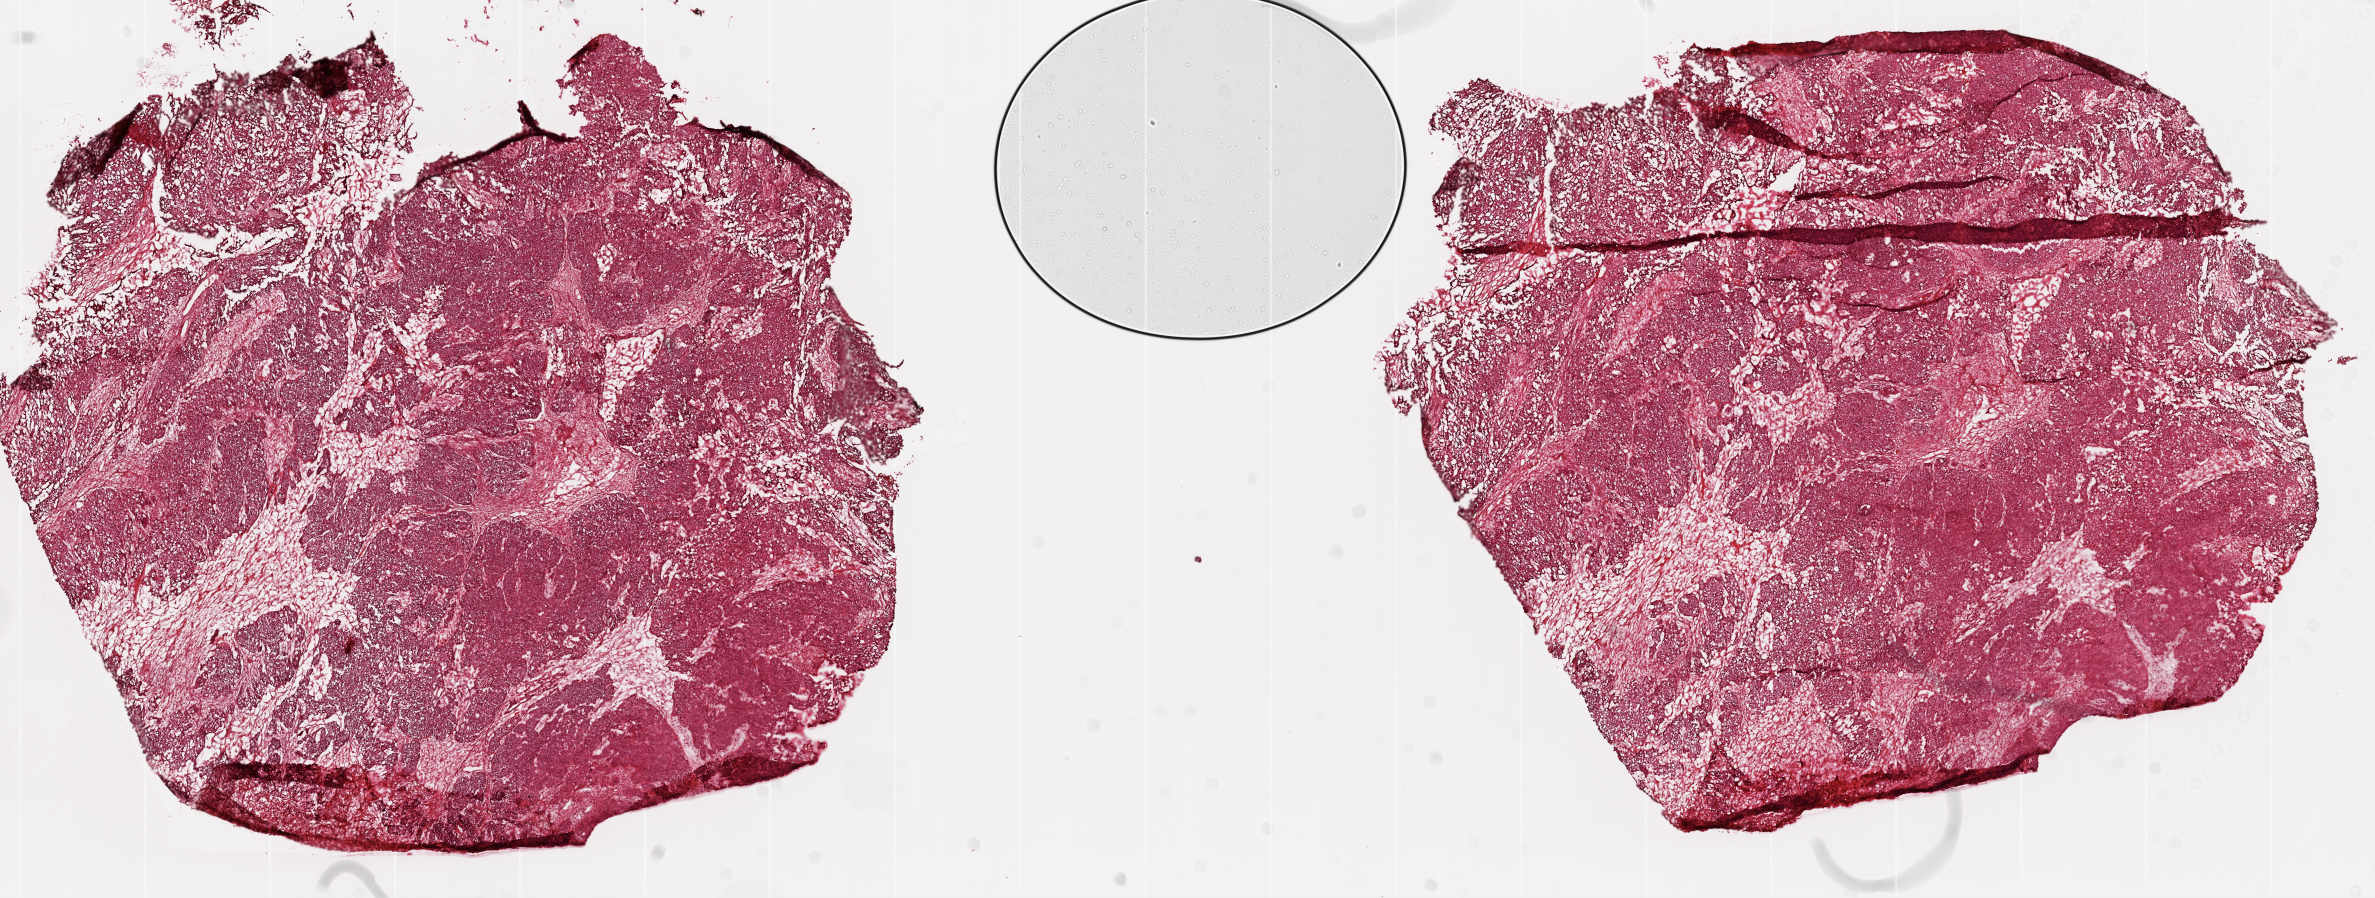
Whole-slide histology image, H&E-stained — whole scanned area (about 19.1 x 7.2 mm, acquisition: 20x scan) shown as a low-resolution overview; frozen section from the top of the tissue portion; ovary, primary tumour sample. Female patient; age at initial diagnosis 43 years. Histologic grade: G3 (poorly differentiated). Pathologist review of this section (percent, as recorded): tumour cells 89%, tumour nuclei 90%, normal cells 0%, stromal cells 10%, necrosis 1%.
• pathologic diagnosis: Serous cystadenocarcinoma, NOS
• FIGO stage: IIIC